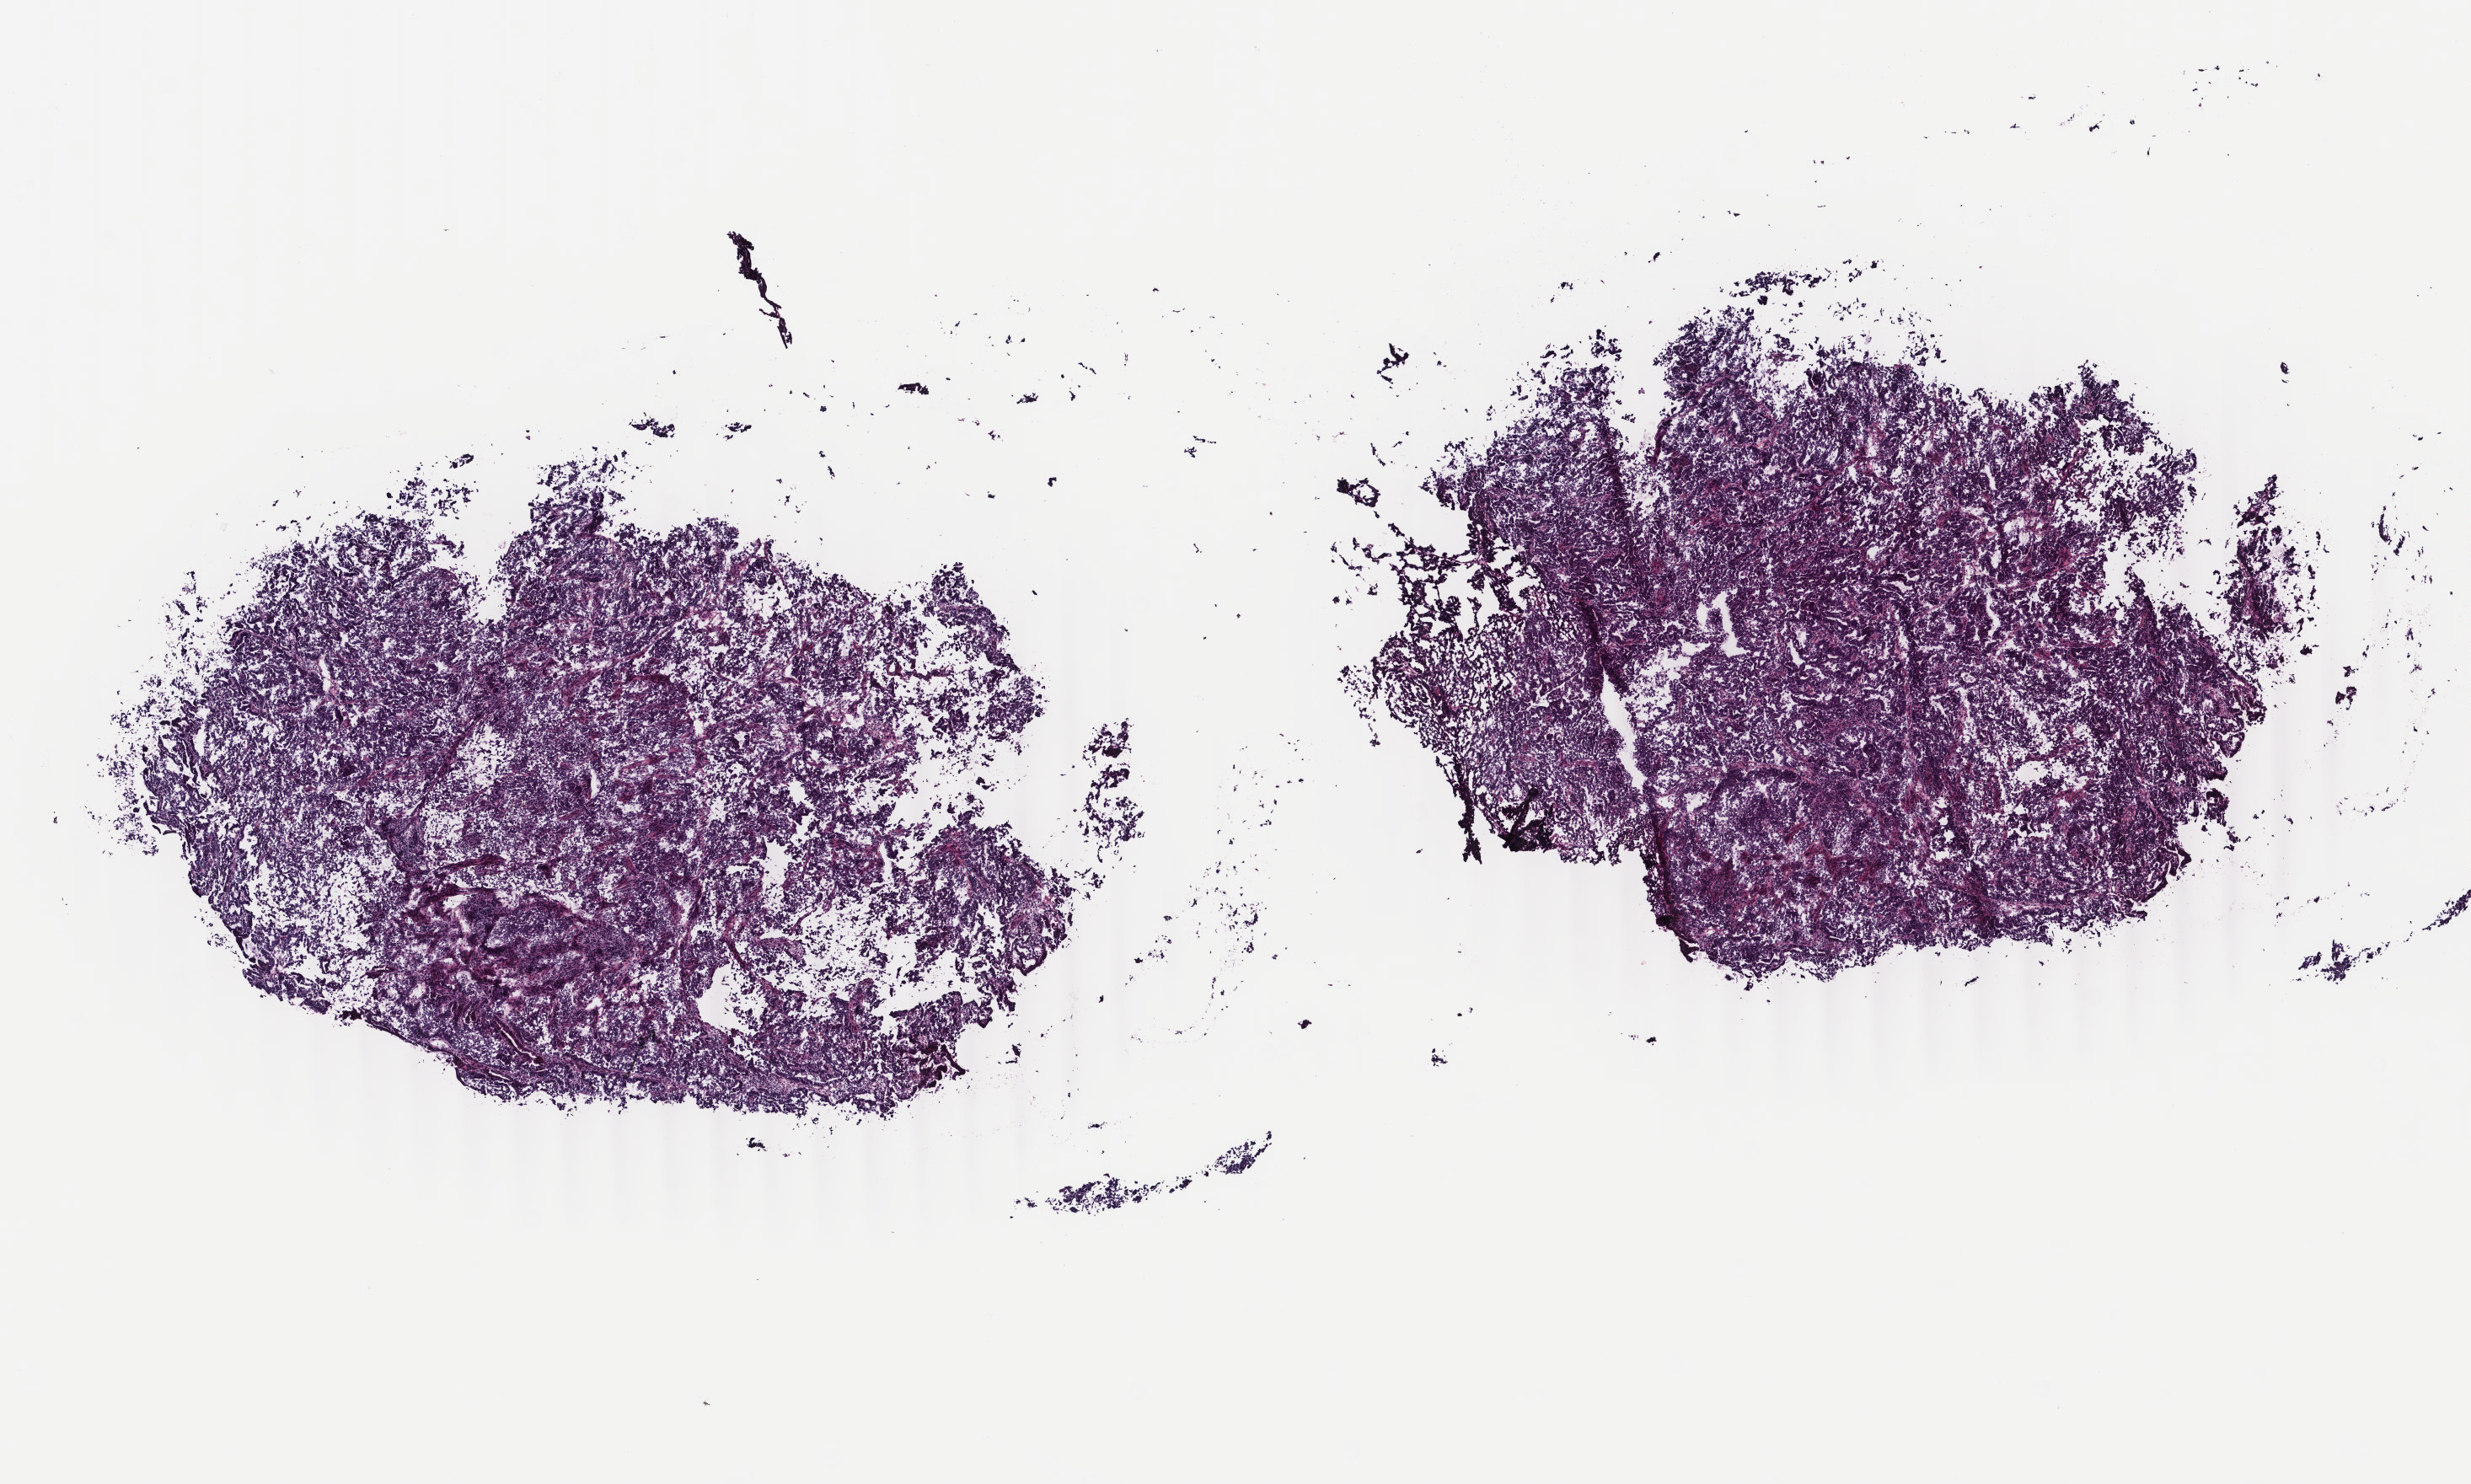
Whole-slide histology image, Hematoxylin and eosin (H&E) stained, shown as a low-resolution overview of the whole scanned area (about 11.7 x 7.0 mm). Frozen section. Uterus, primary tumour sample. Female, age 68 years at initial diagnosis. Histologic grade: G1 (well differentiated). Slide review estimates, as recorded: tumour cells 100%, tumour nuclei 85%, normal cells 0%, stromal cells 0%, necrosis 0%. Infiltration values recorded for this section: lymphocyte infiltration 0%, monocyte infiltration 0%, neutrophil infiltration 0%.
FIGO stage: IA. Histologic diagnosis: Endometrioid adenocarcinoma, NOS (endometrium).